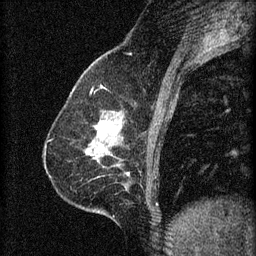
Breast MRI (dynamic contrast-enhanced), one sagittal slice. Slice 24 of 60 in the series (ordered by position). 3 images stored at this slice position (order not interpretable as contrast timing). 1.5 T. TE 4.2 ms, TR 8.2 ms. 256 × 256 image matrix, field of view 180 × 180 mm. Female patient, age 59 years.
Outlined on this slice (semi-automatic segmentation, software-assisted and operator-edited):
- analysis volume of interest (the breast-tissue region the enhancement analysis was run in; not a lesion): bounding box (x1, y1, x2, y2) in pixels: (67, 104, 126, 161)
- tumour enhancement mask (voxels above the 70 % enhancement threshold inside the analysis volume of interest): (93, 122, 112, 145)